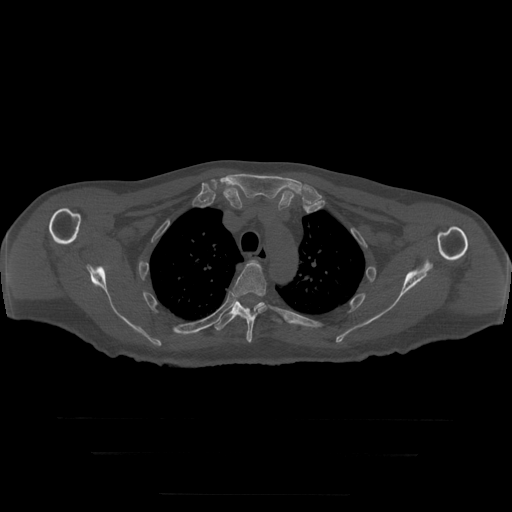
CT including the spine, one axial slice. Position 237 of 397 along the scan axis. Reconstruction kernel STANDARD. 120 kVp. Bone window (W 1800 / L 400 HU). 1.25 mm slice thickness. 512 × 512 image matrix, field of view 510 × 510 mm. Patient age 73 years. From the clinical record (not read from this slice): primary cancer: prostate.
Structures marked on this image (semi-automatically segmented with operator editing):
- T3 vertebra: bounding box [x1, y1, x2, y2] px = [254, 261, 257, 263]
- T4 vertebra: [233, 261, 266, 343]
- T5 vertebra: [215, 301, 281, 333]